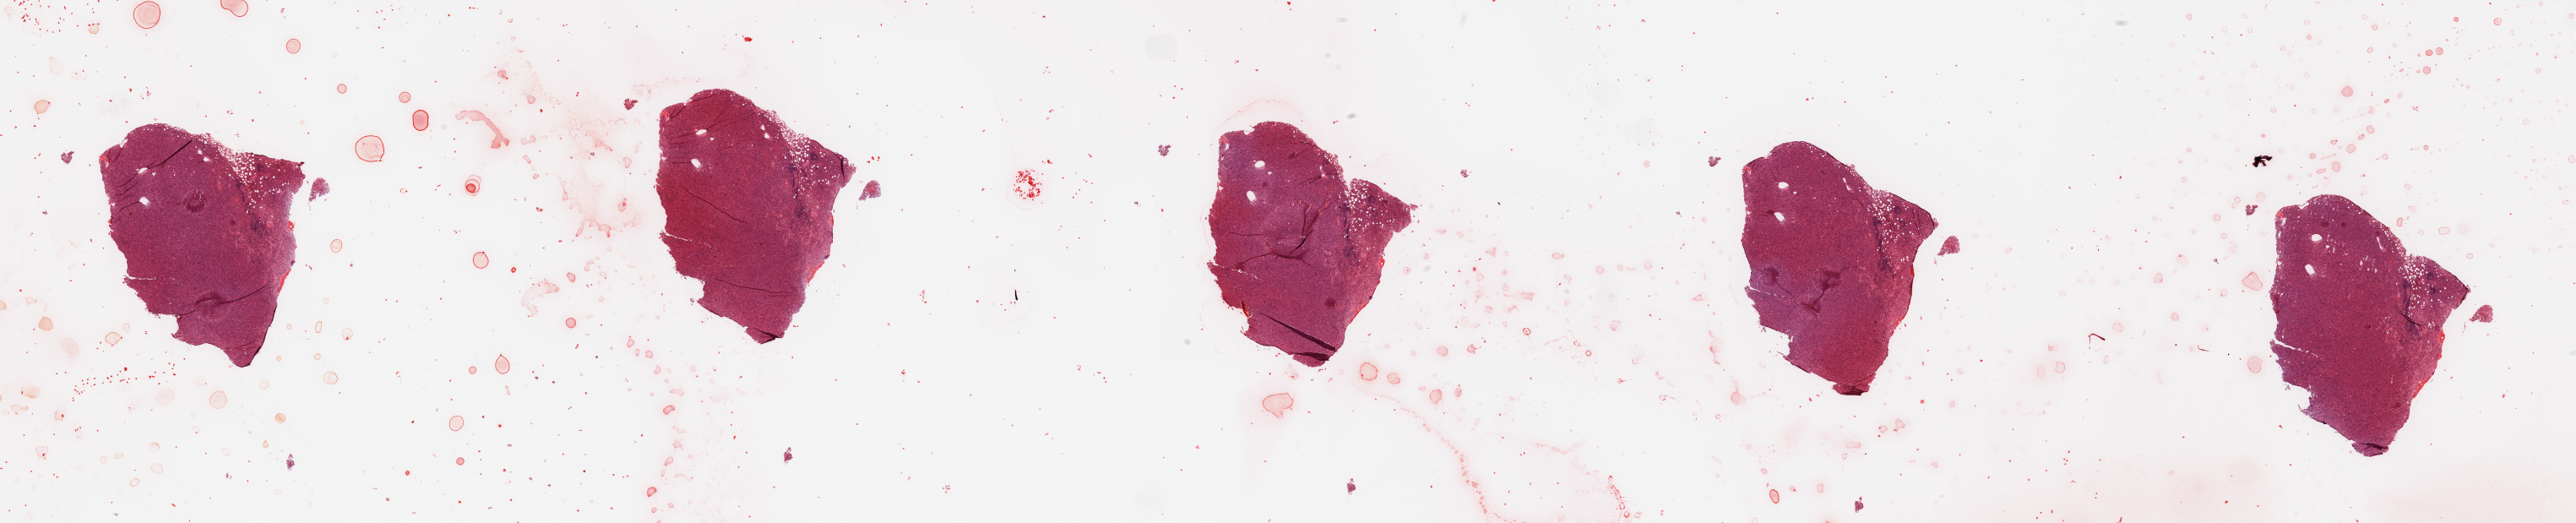
H&E whole-slide image — a low-resolution overview of the entire scanned area, about 48.2 x 9.8 mm (slide scanned at 20x). Tumour tissue sample. 75-year-old female patient.
Patient diagnosis (cohort enrolment): sarcoma (site not recorded at cohort level). Primary tumour site (as recorded): lower extremity.